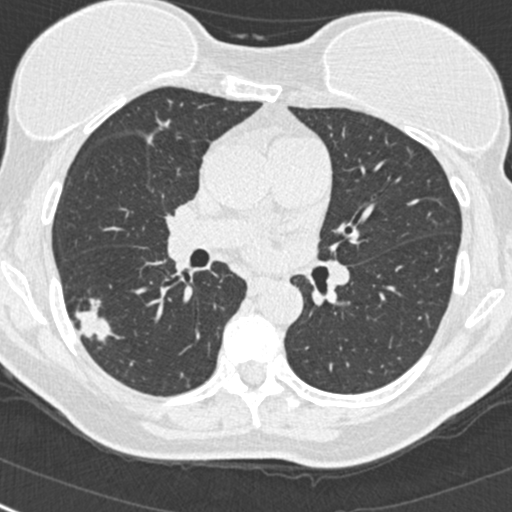
Low-dose screening chest CT, one axial slice; position 145 of 268 along the scan axis; reconstruction kernel B30f; lung window (W 1500 / L -600 HU); 1 mm slice thickness; 512 × 512 image matrix.
Outlined on this slice (outlined manually by an expert reader):
- lesion 1 (tumor, upper lobe of right lung): bounding box (x1, y1, x2, y2) in pixels: (75, 299, 111, 341)